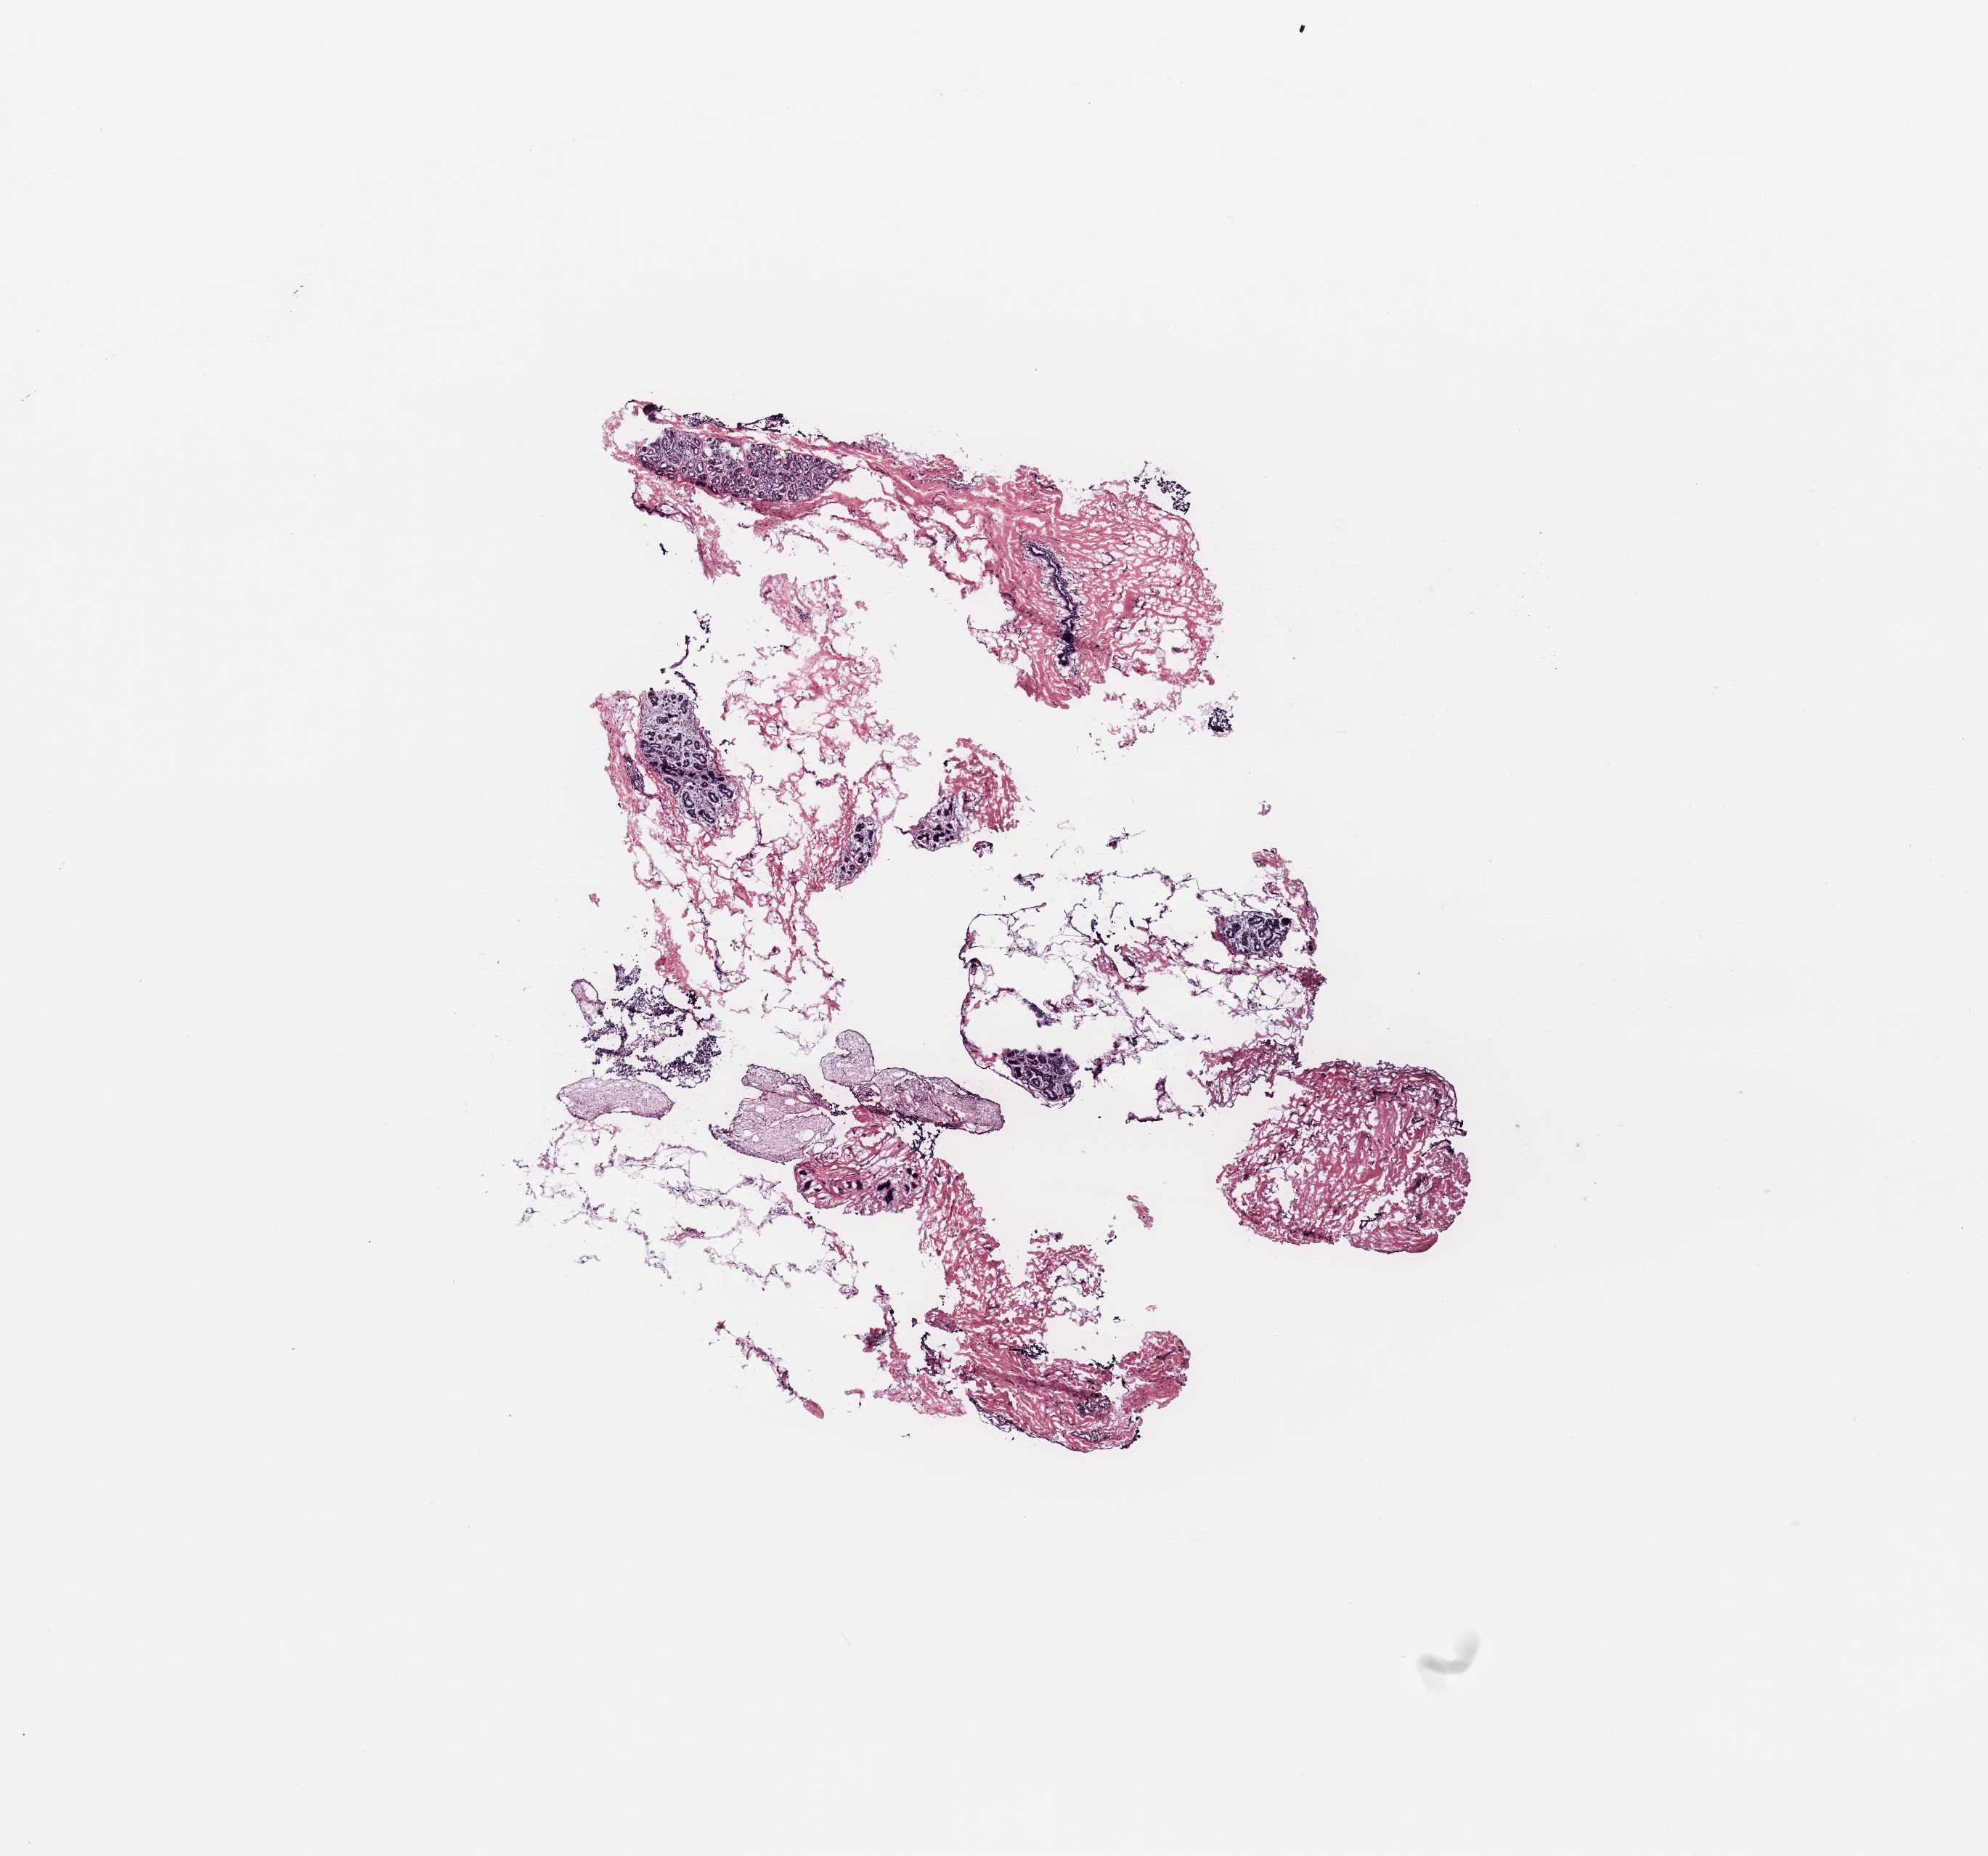
Whole-slide histology image, Hematoxylin and eosin (H&E) stained — a low-resolution overview of the entire scanned area, about 10.8 x 10.1 mm (acquisition: 20x scan); breast, tissue type not recorded.
Patient diagnosis (cohort enrolment): breast cancer (breast).